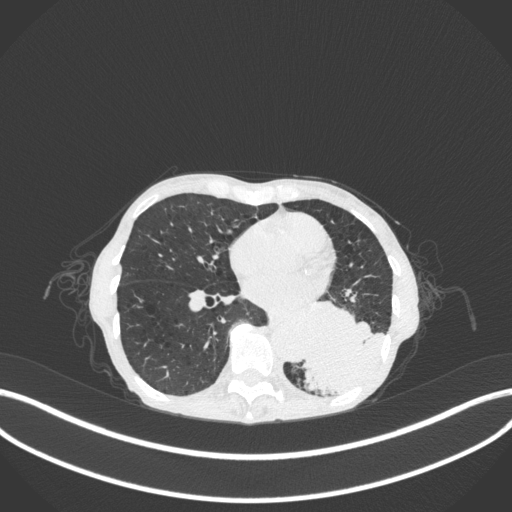
Chest CT, one axial slice; slice 111 of 347 in the series (ordered by position); 120 kVp; lung window (W 1500 / L -600 HU); 1 mm slice thickness; 512 × 512 image matrix, field of view 400 × 400 mm. Female patient, age 70 years. Case-level facts recorded for this patient, not image findings: clinical TNM (as recorded): T3 N0 M0.
Outlined on this slice (rectangle marked by the reading radiologist):
- lung tumour (recorded histology: small cell carcinoma): bounding box <298,288,387,400> (left, top, right, bottom; pixels)